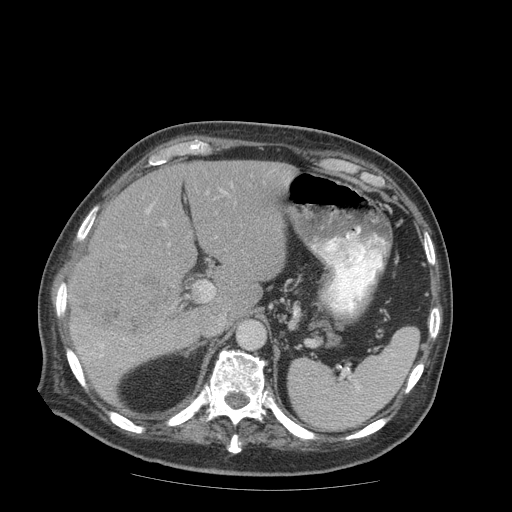
Contrast-enhanced abdominal CT (liver protocol), one axial slice. Position 55 of 99 along the scan axis. Reconstruction kernel STANDARD. Soft-tissue window (W 400 / L 40 HU). 2.5 mm slice thickness. 512 × 512 image matrix. From the clinical record (not read from this slice): diagnosis: hepatocellular carcinoma (patient treated with transarterial chemoembolisation; whether this scan precedes or follows treatment is not stated here); TNM stage (as recorded): Stage-IIIB; Child-Pugh class: A; tumour differentiation: well differentiated; tumour nodularity: multinodular.
Structures marked on this image (semi-automatic segmentation, software-assisted and operator-edited):
- liver parenchyma outside the tumour (the mass and vessels are separate outlines, so this box may not span the whole liver): bounding box [x1, y1, x2, y2] px = [66, 160, 296, 402]
- mass: [72, 247, 179, 340]
- liver vessels: [81, 205, 152, 357]